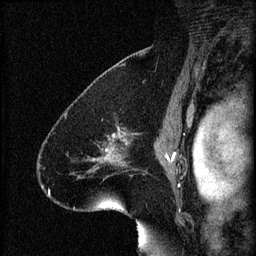
Breast MRI (dynamic contrast-enhanced), one sagittal slice. Position 45 of 60 along the scan axis. 3 images stored at this slice position (order not interpretable as contrast timing). 1.5 T. TE 4.2 ms, TR 8.2 ms. 2 mm slice thickness. 256 × 256 image matrix, field of view 180 × 180 mm. Female patient, age 41 years.
Annotated regions visible in this slice (semi-automatically segmented with operator editing):
- analysis volume of interest (the breast-tissue region the enhancement analysis was run in; not a lesion): bounding box (x1, y1, x2, y2) in pixels: (74, 128, 134, 181)
- tumour enhancement mask (voxels above the 70 % enhancement threshold inside the analysis volume of interest): (94, 128, 122, 161)